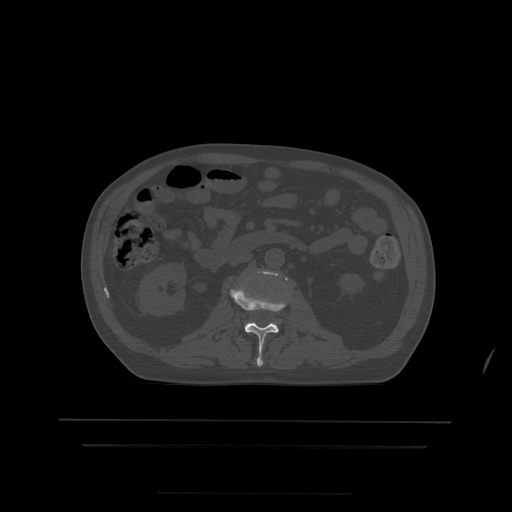
CT including the spine, one axial slice. Slice 139 of 522 in the series (ordered by position). Bone window (W 1800 / L 400 HU). 1.25 mm slice thickness. 512 × 512 image matrix, field of view 436 × 436 mm. Patient age 68 years. From the clinical record (not read from this slice): primary cancer: urothelial.
Annotated regions visible in this slice (semi-automatic segmentation, software-assisted and operator-edited):
- L2 vertebra: bounding box (x1, y1, x2, y2) in pixels: (230, 286, 286, 367)
- L3 vertebra: (260, 271, 288, 303)